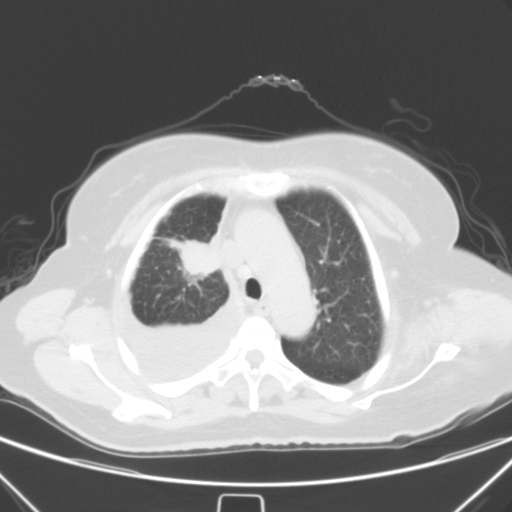
Chest CT, one axial slice. Slice 43 of 55 in the series (ordered by position). 120 kVp. Lung window (W 1500 / L -600 HU). 5 mm slice thickness. 512 × 512 image matrix. Female patient, age 66 years. Case-level facts recorded for this patient, not image findings: clinical TNM (as recorded): T2 N0 M1.
Structures marked on this image (rectangle marked by the reading radiologist):
- lung tumour (recorded histology: adenocarcinoma): bounding box (x1, y1, x2, y2) in pixels: (171, 235, 220, 286)